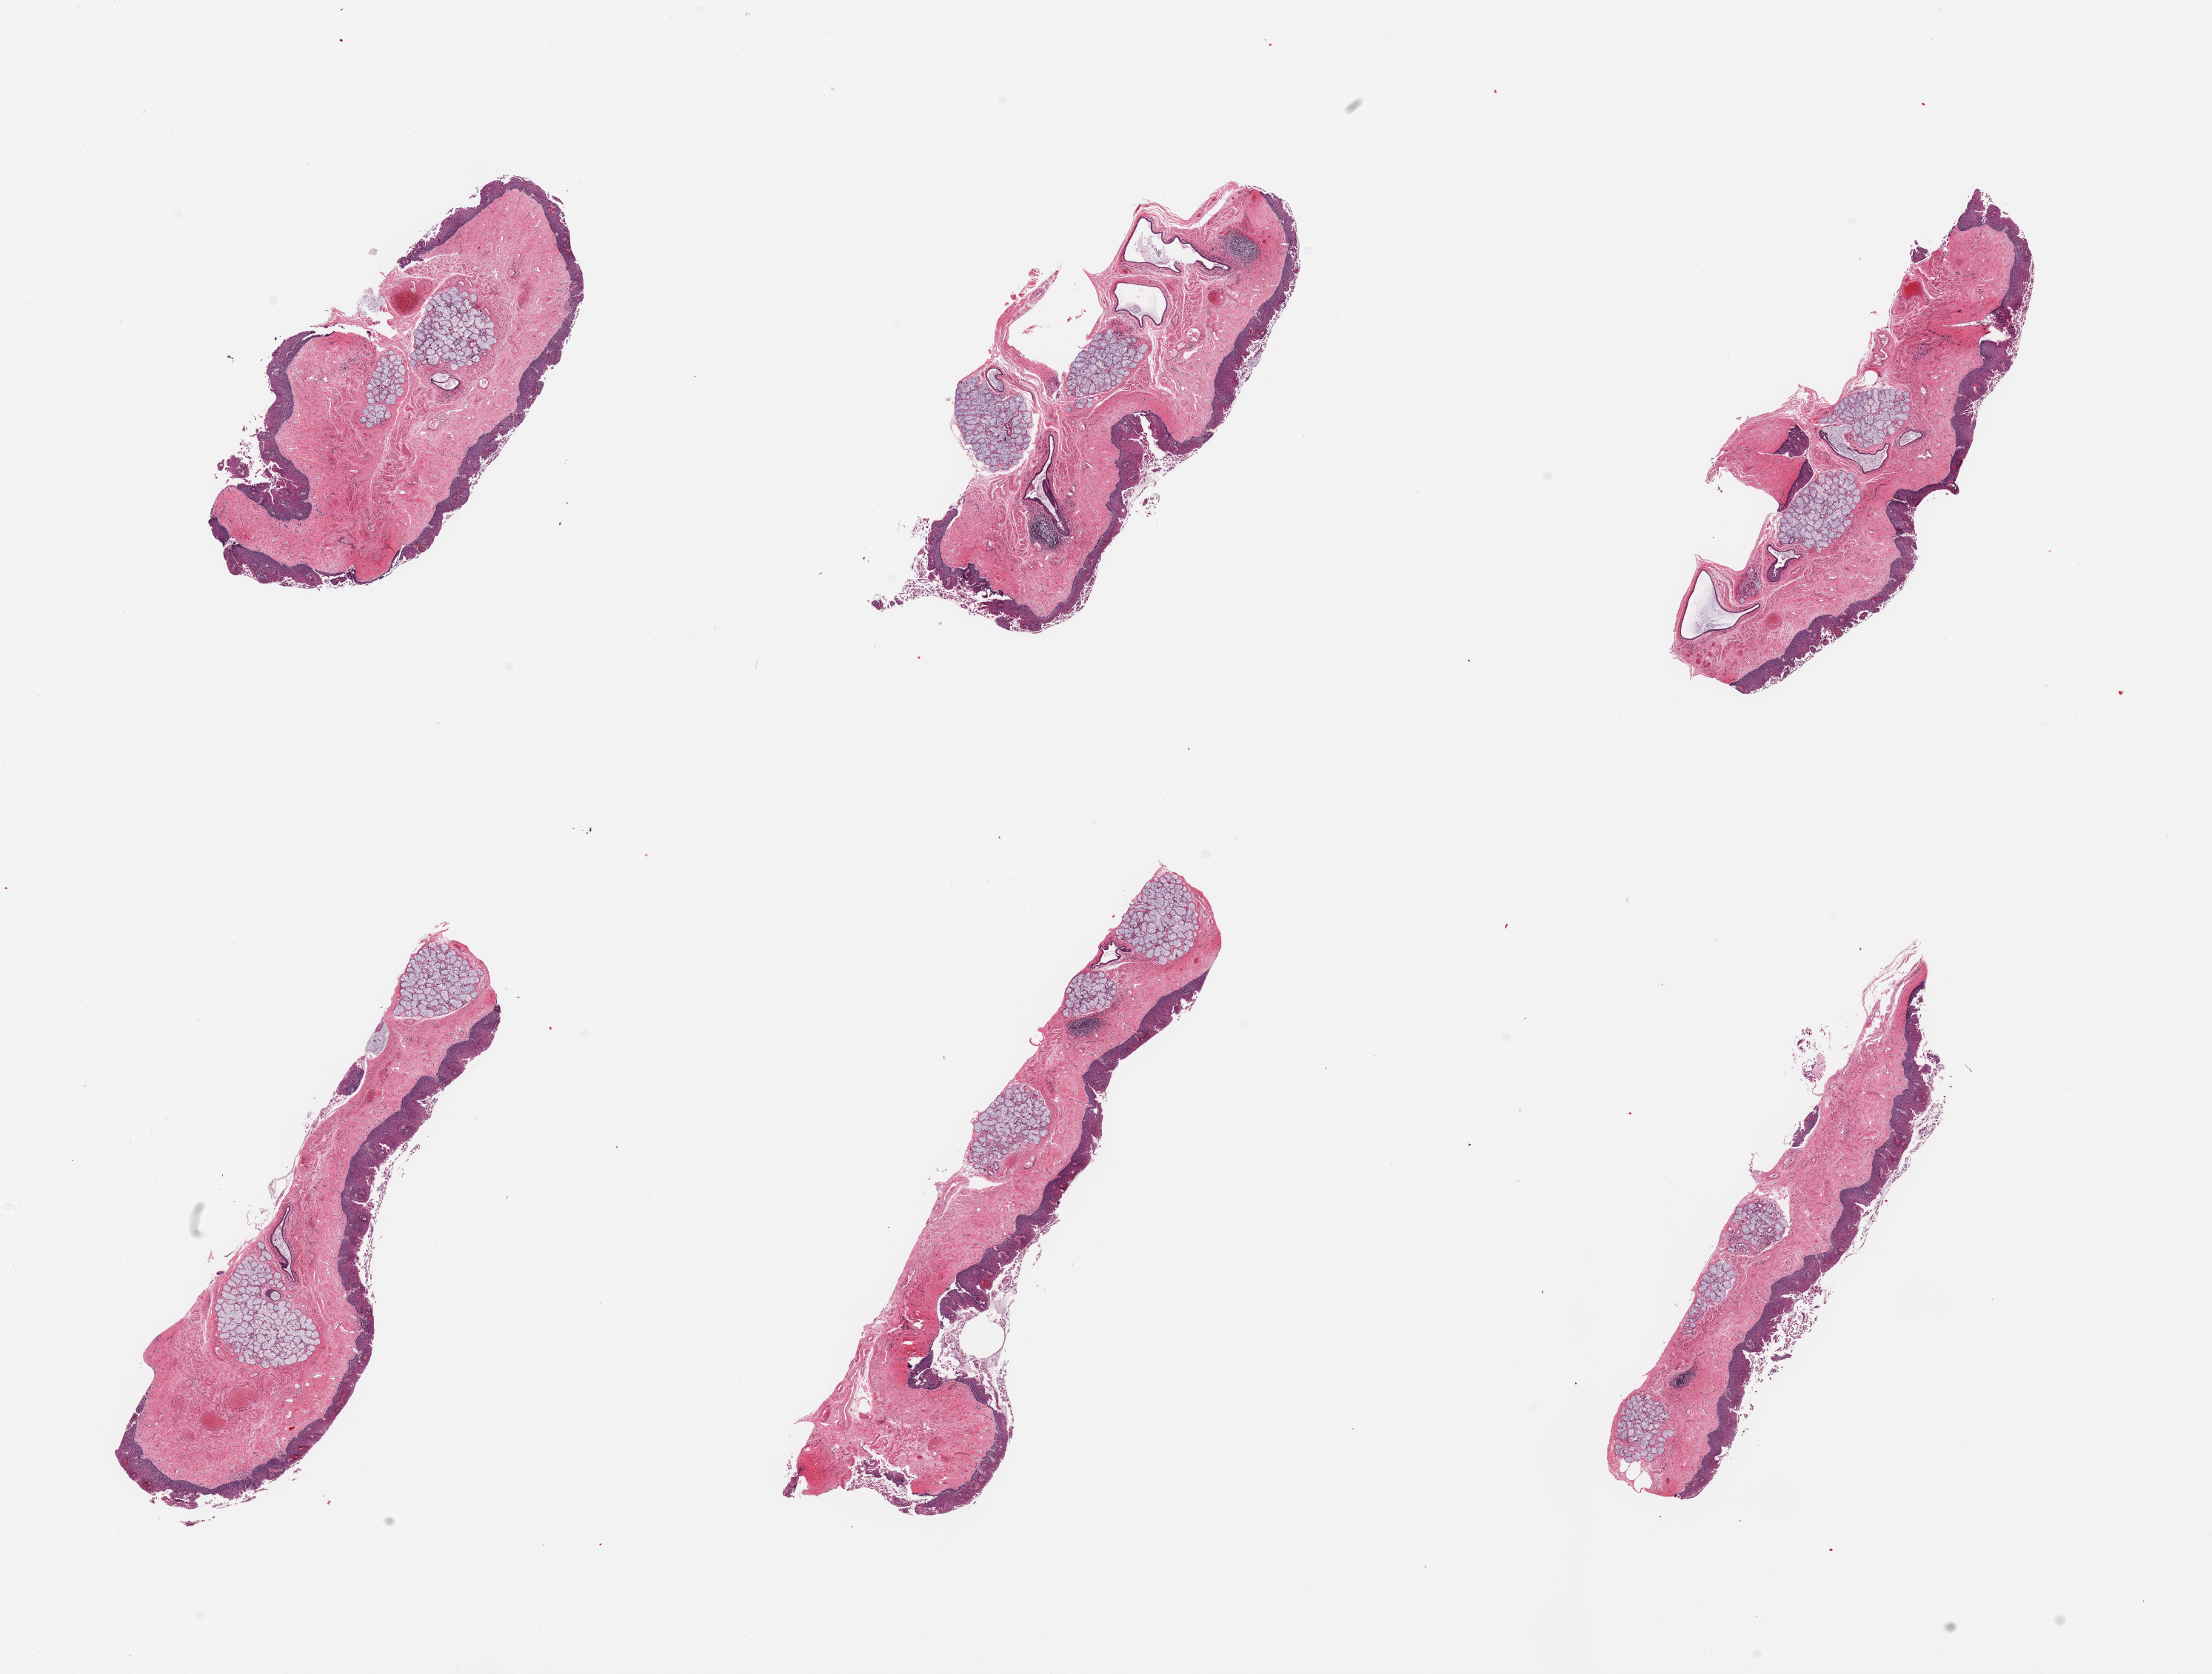
Hematoxylin and eosin (H&E) whole-slide image — whole scanned area (about 23.6 x 17.9 mm, slide scanned at 20x) shown as a low-resolution overview, PAXgene-fixed, paraffin-embedded tissue, section of esophageal mucous membrane (target tissue), tissue donor sample. Male donor.
- review note (as recorded): 6 pieces; some sloughing of squamous epithelium, numerous clusters of submucosal glands, few dilated ducts (pseudodiverticulosis)